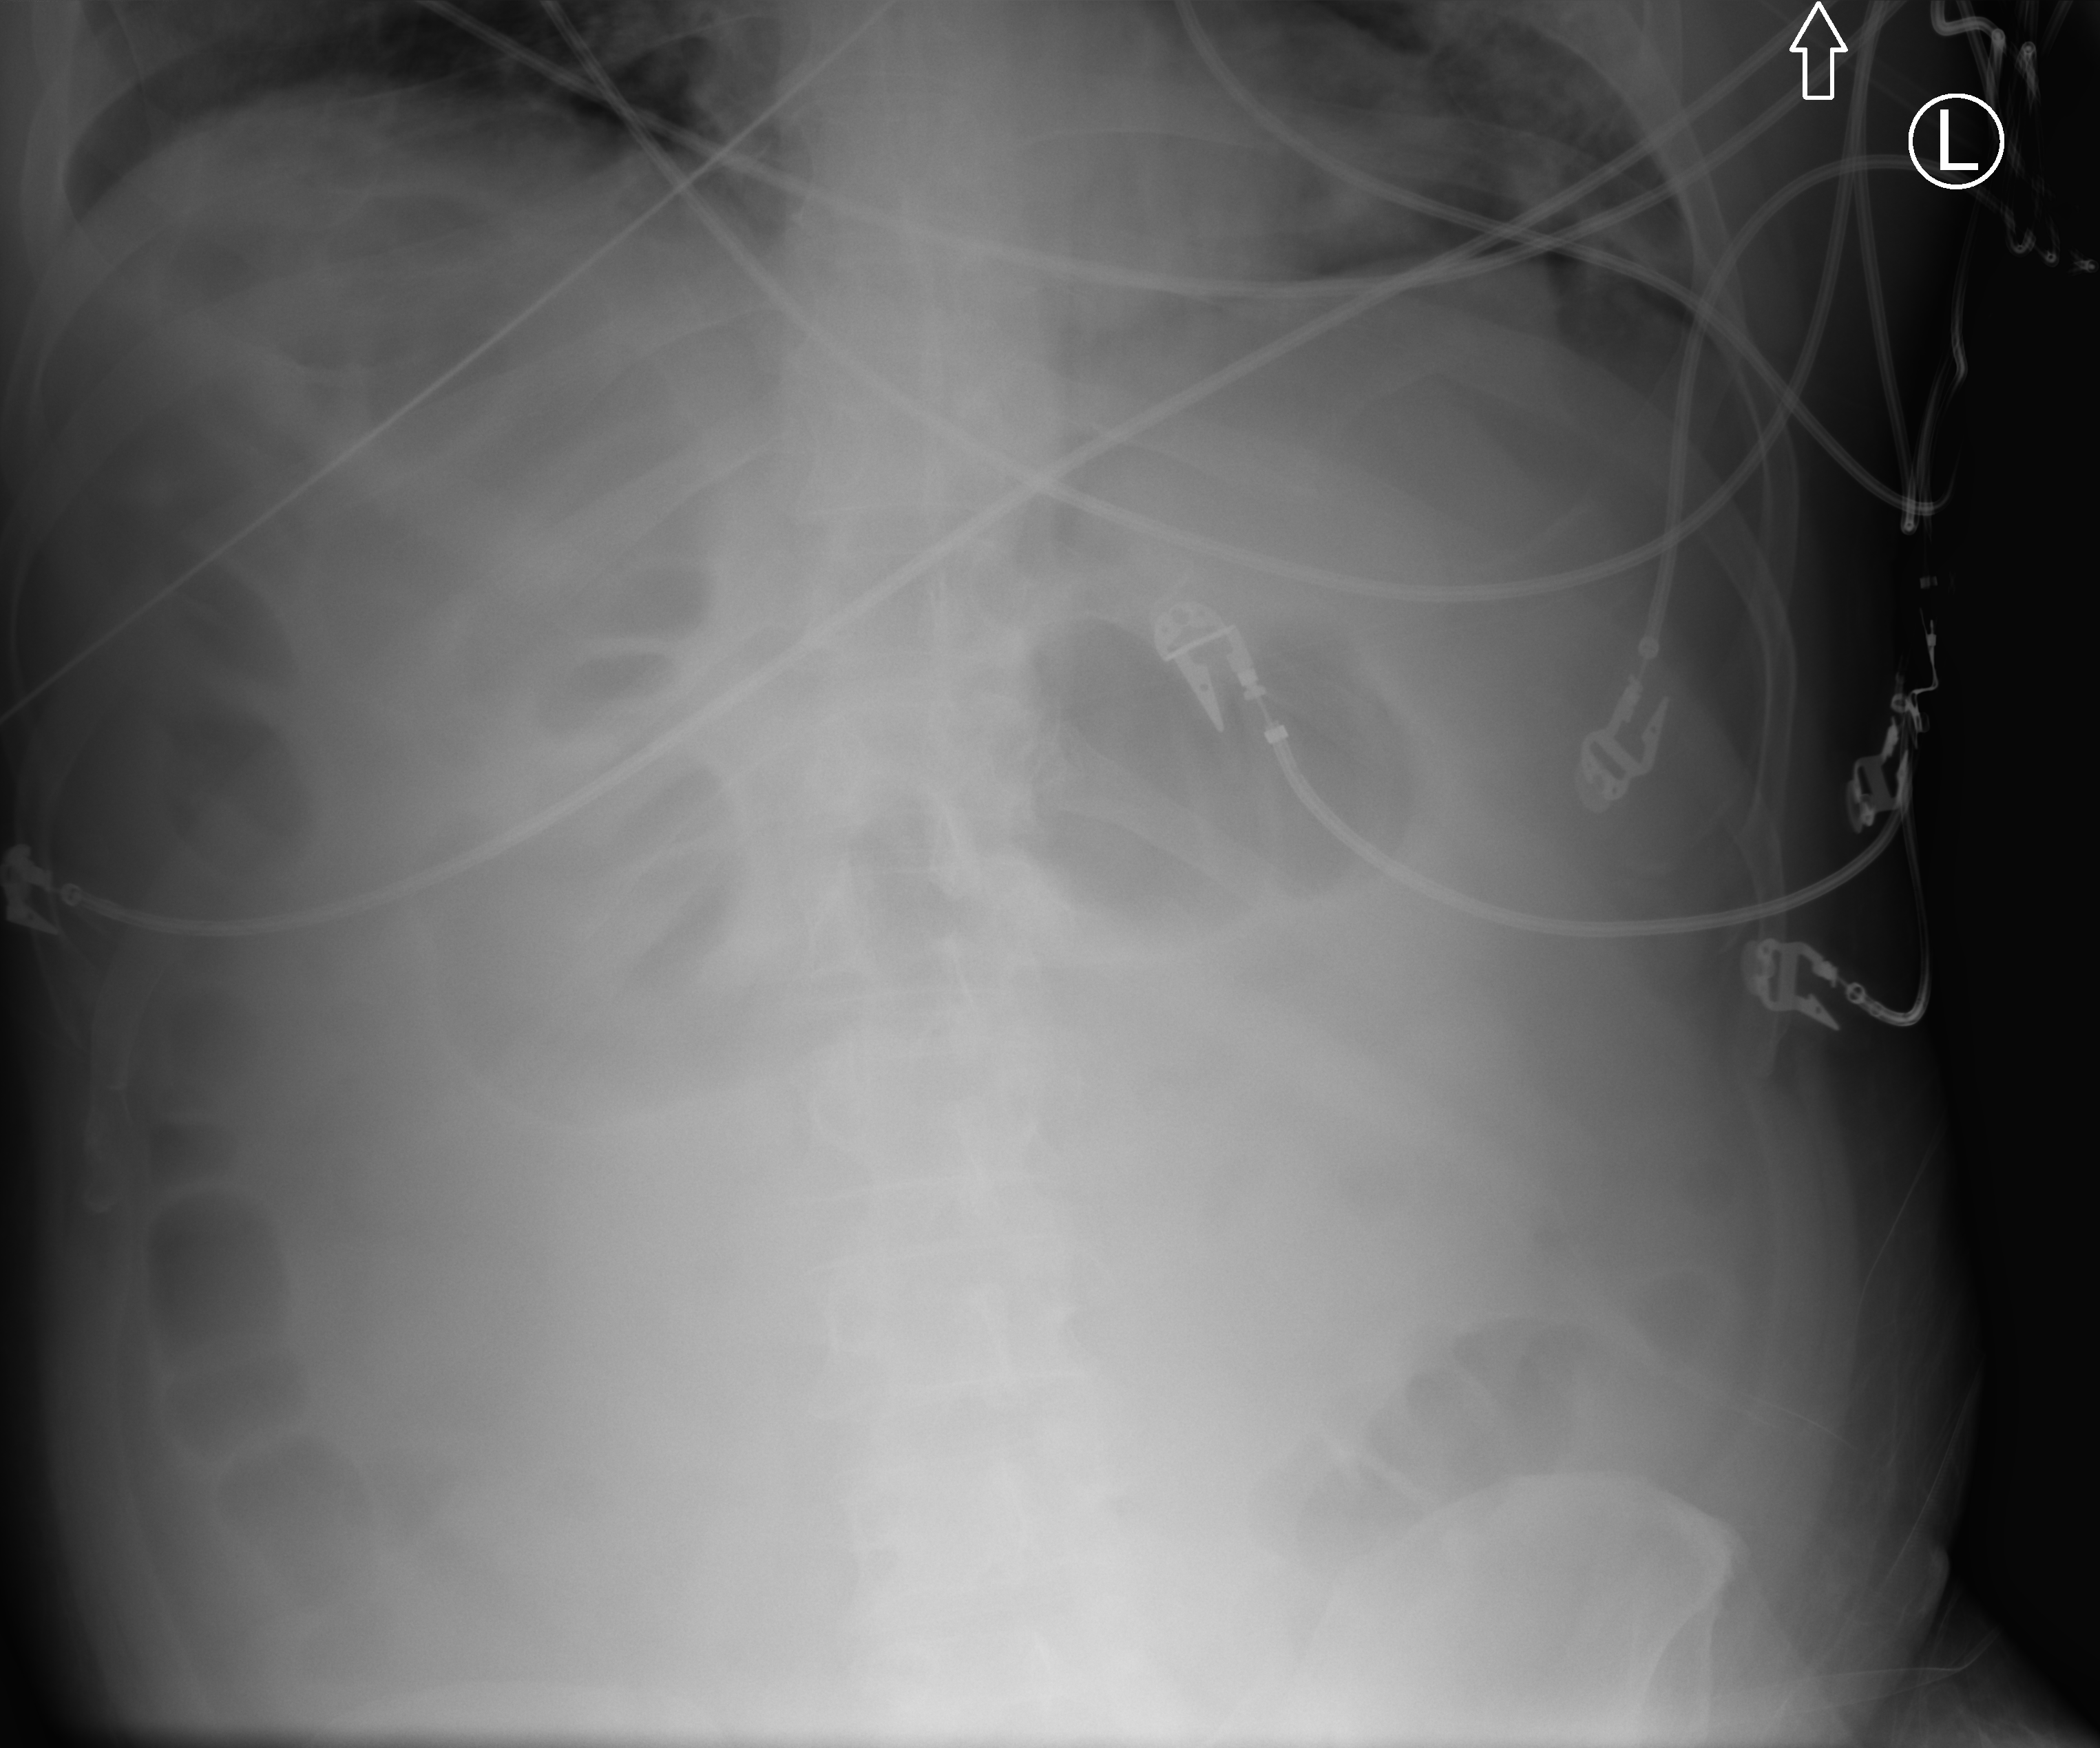
Portable abdomen radiograph. Male patient hospitalised with COVID-19, age 18–59 years.
From the hospital-stay record, not from the radiograph (when in the stay this image was taken is not recorded): hypertension (admission record): no; COPD (admission record): no; mechanically ventilated during this hospital stay: yes.